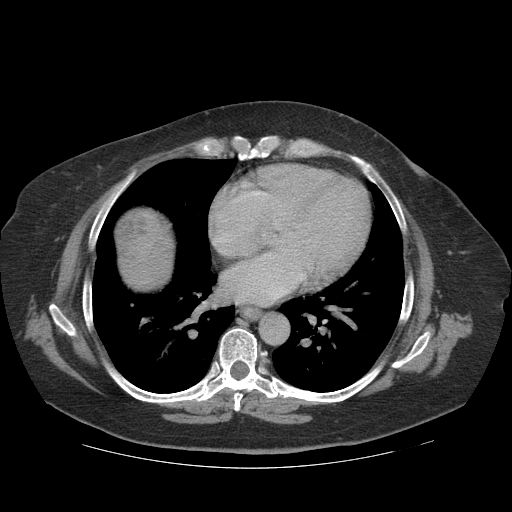
Contrast-enhanced abdominal CT (liver protocol), one axial slice; position 112 of 121 along the scan axis; soft-tissue window (W 400 / L 40 HU); 2.5 mm slice thickness; 512 × 512 image matrix, field of view 420 × 420 mm. From the clinical record (not read from this slice): diagnosis: hepatocellular carcinoma (patient treated with transarterial chemoembolisation; whether this scan precedes or follows treatment is not stated here); TNM stage (as recorded): Stage-IIIA; Child-Pugh class: A.
Outlined on this slice (semi-automatically segmented with operator editing):
- liver parenchyma outside the tumour (the mass and vessels are separate outlines, so this box may not span the whole liver): box from (x=114, y=208) to (x=172, y=288) px
- mass: (x=116, y=216)–(x=146, y=246)